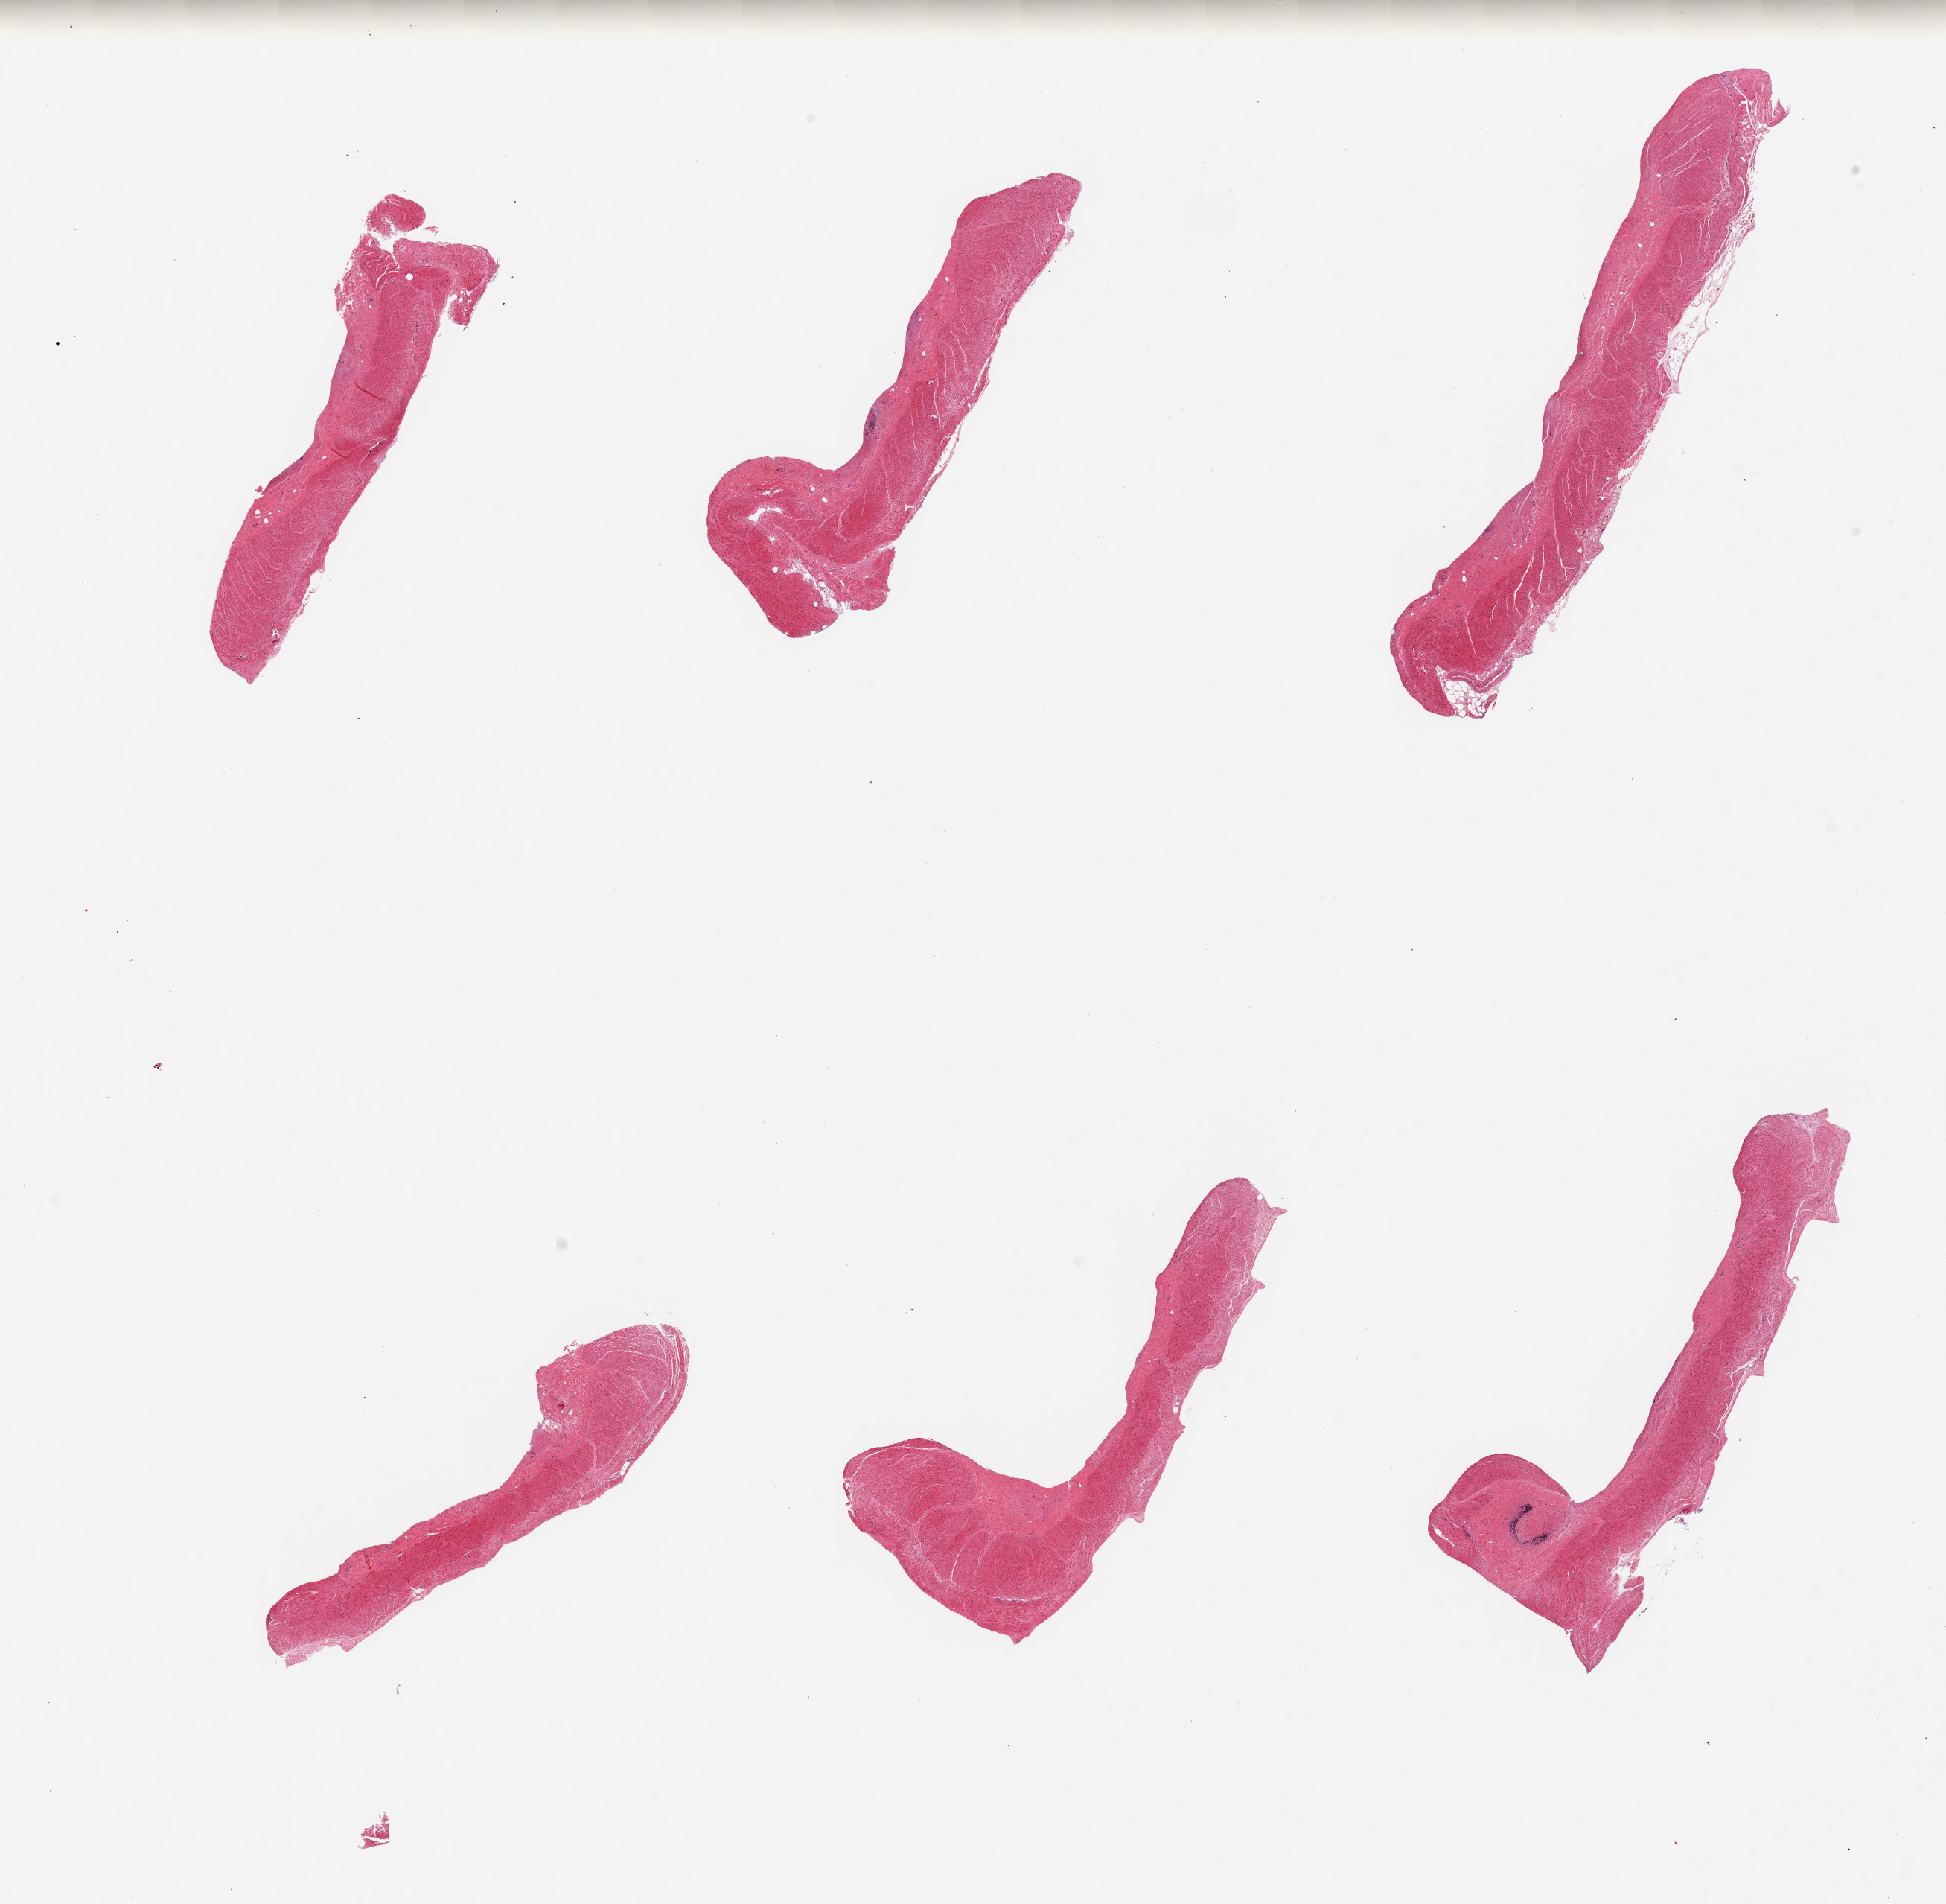
Hematoxylin and eosin (H&E) whole-slide image, brightfield — whole scanned area (about 20.7 x 20.2 mm) shown as a low-resolution overview; PAXgene-fixed, paraffin-embedded tissue; section of sigmoid colon (target tissue); tissue donor sample. Donor: female.
Pathologist's review note for this sample: 6 pieces, predominantly well trimmed, ? focus of residual autolyzed mucosa.